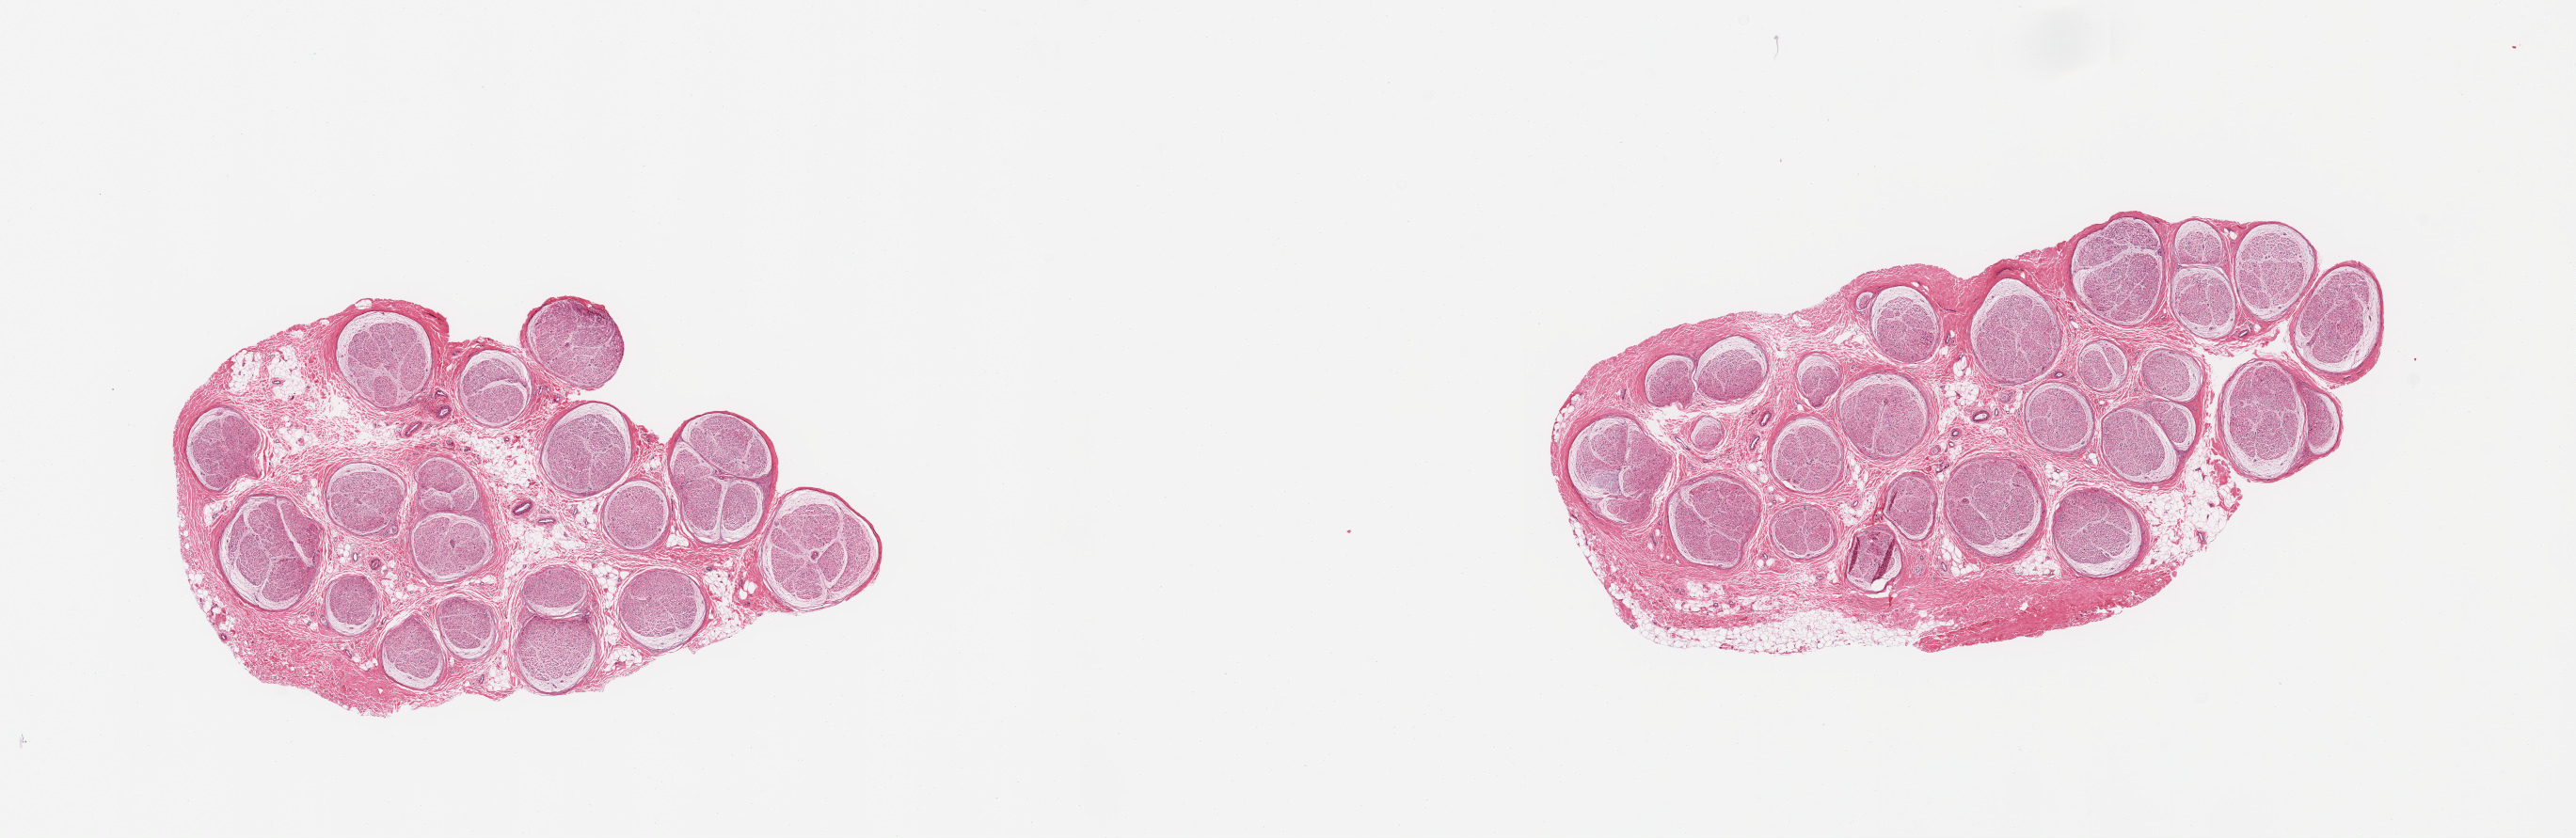
Whole-slide image, H&E stain — shown as a low-resolution overview of the whole scanned area (about 21.7 x 7.0 mm); PAXgene-fixed, paraffin-embedded tissue; section of tibial nerve (target tissue); donor tissue sample. Donor sex: male.
- reviewer comment on this tissue sample: 2 pieces, no adherent fat